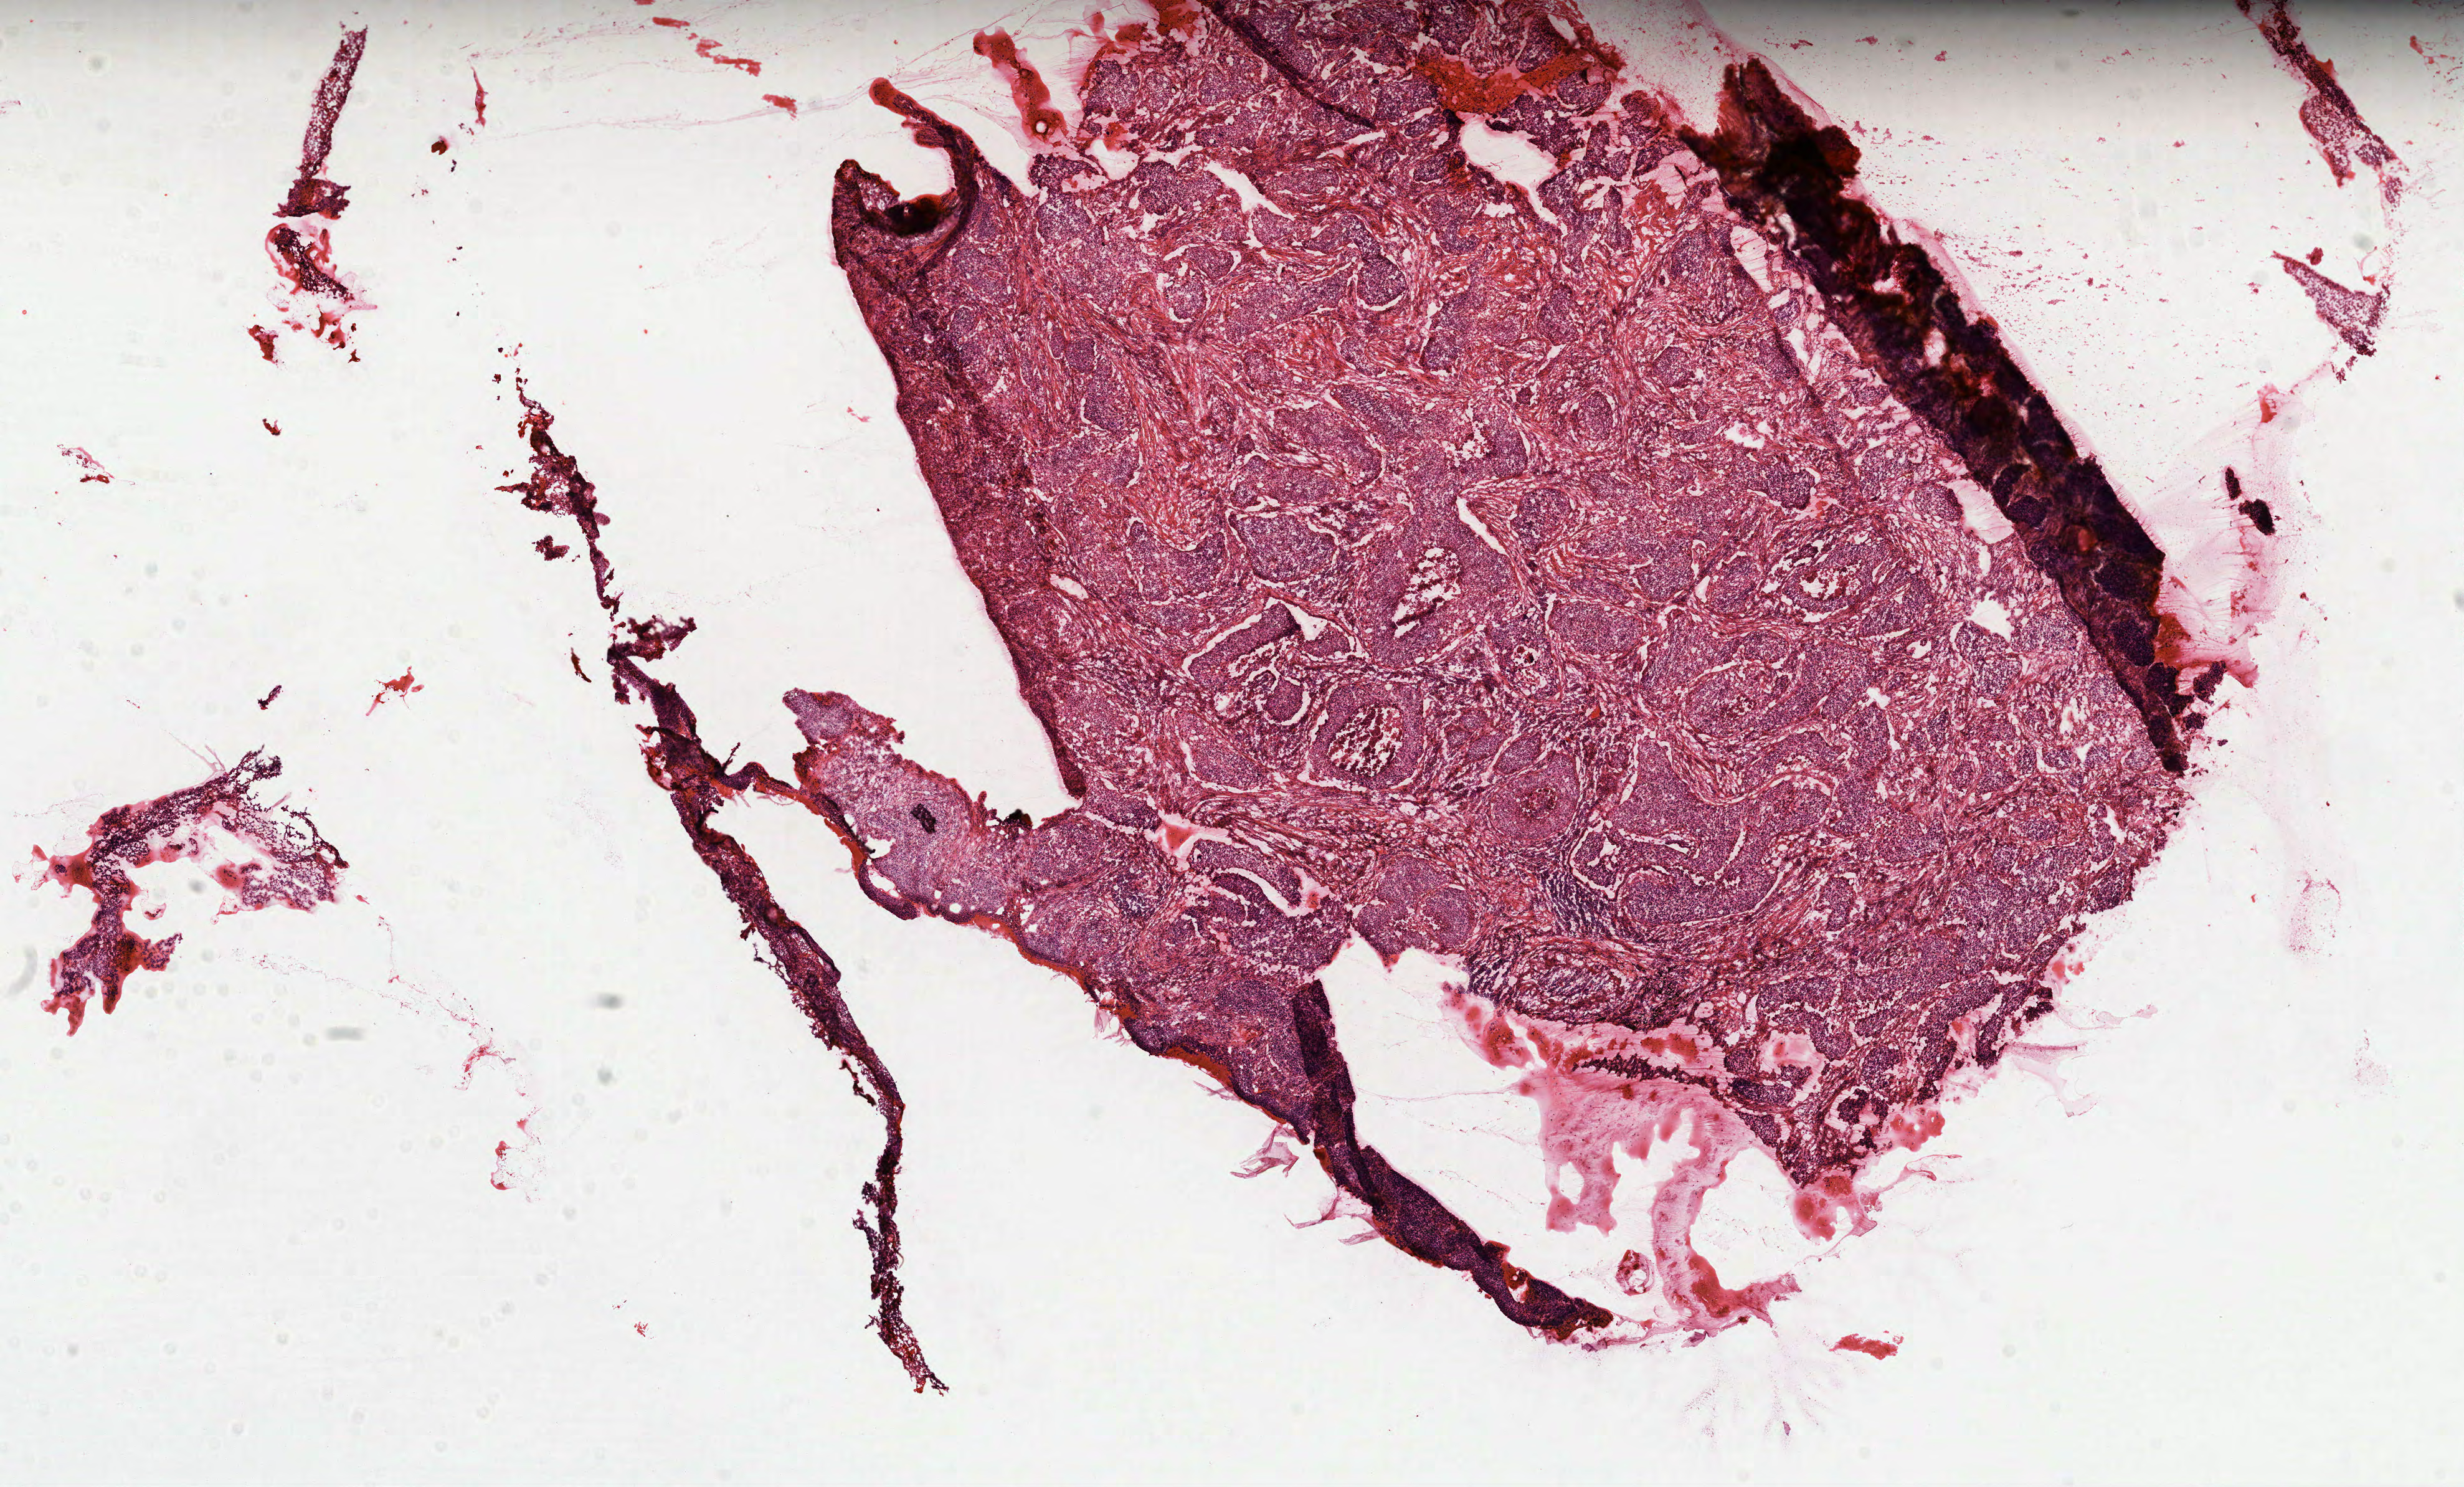
H&E-stained whole-slide image, shown as a low-resolution overview of the whole scanned area (about 16.0 x 9.6 mm, slide scanned at 40x), FFPE section, lung, primary tumour sample. Patient: male, age at initial diagnosis 61 years.
Diagnosis: Squamous cell carcinoma, NOS (lower lobe, lung). TNM: T2 N0 M0. AJCC pathologic stage: IB.